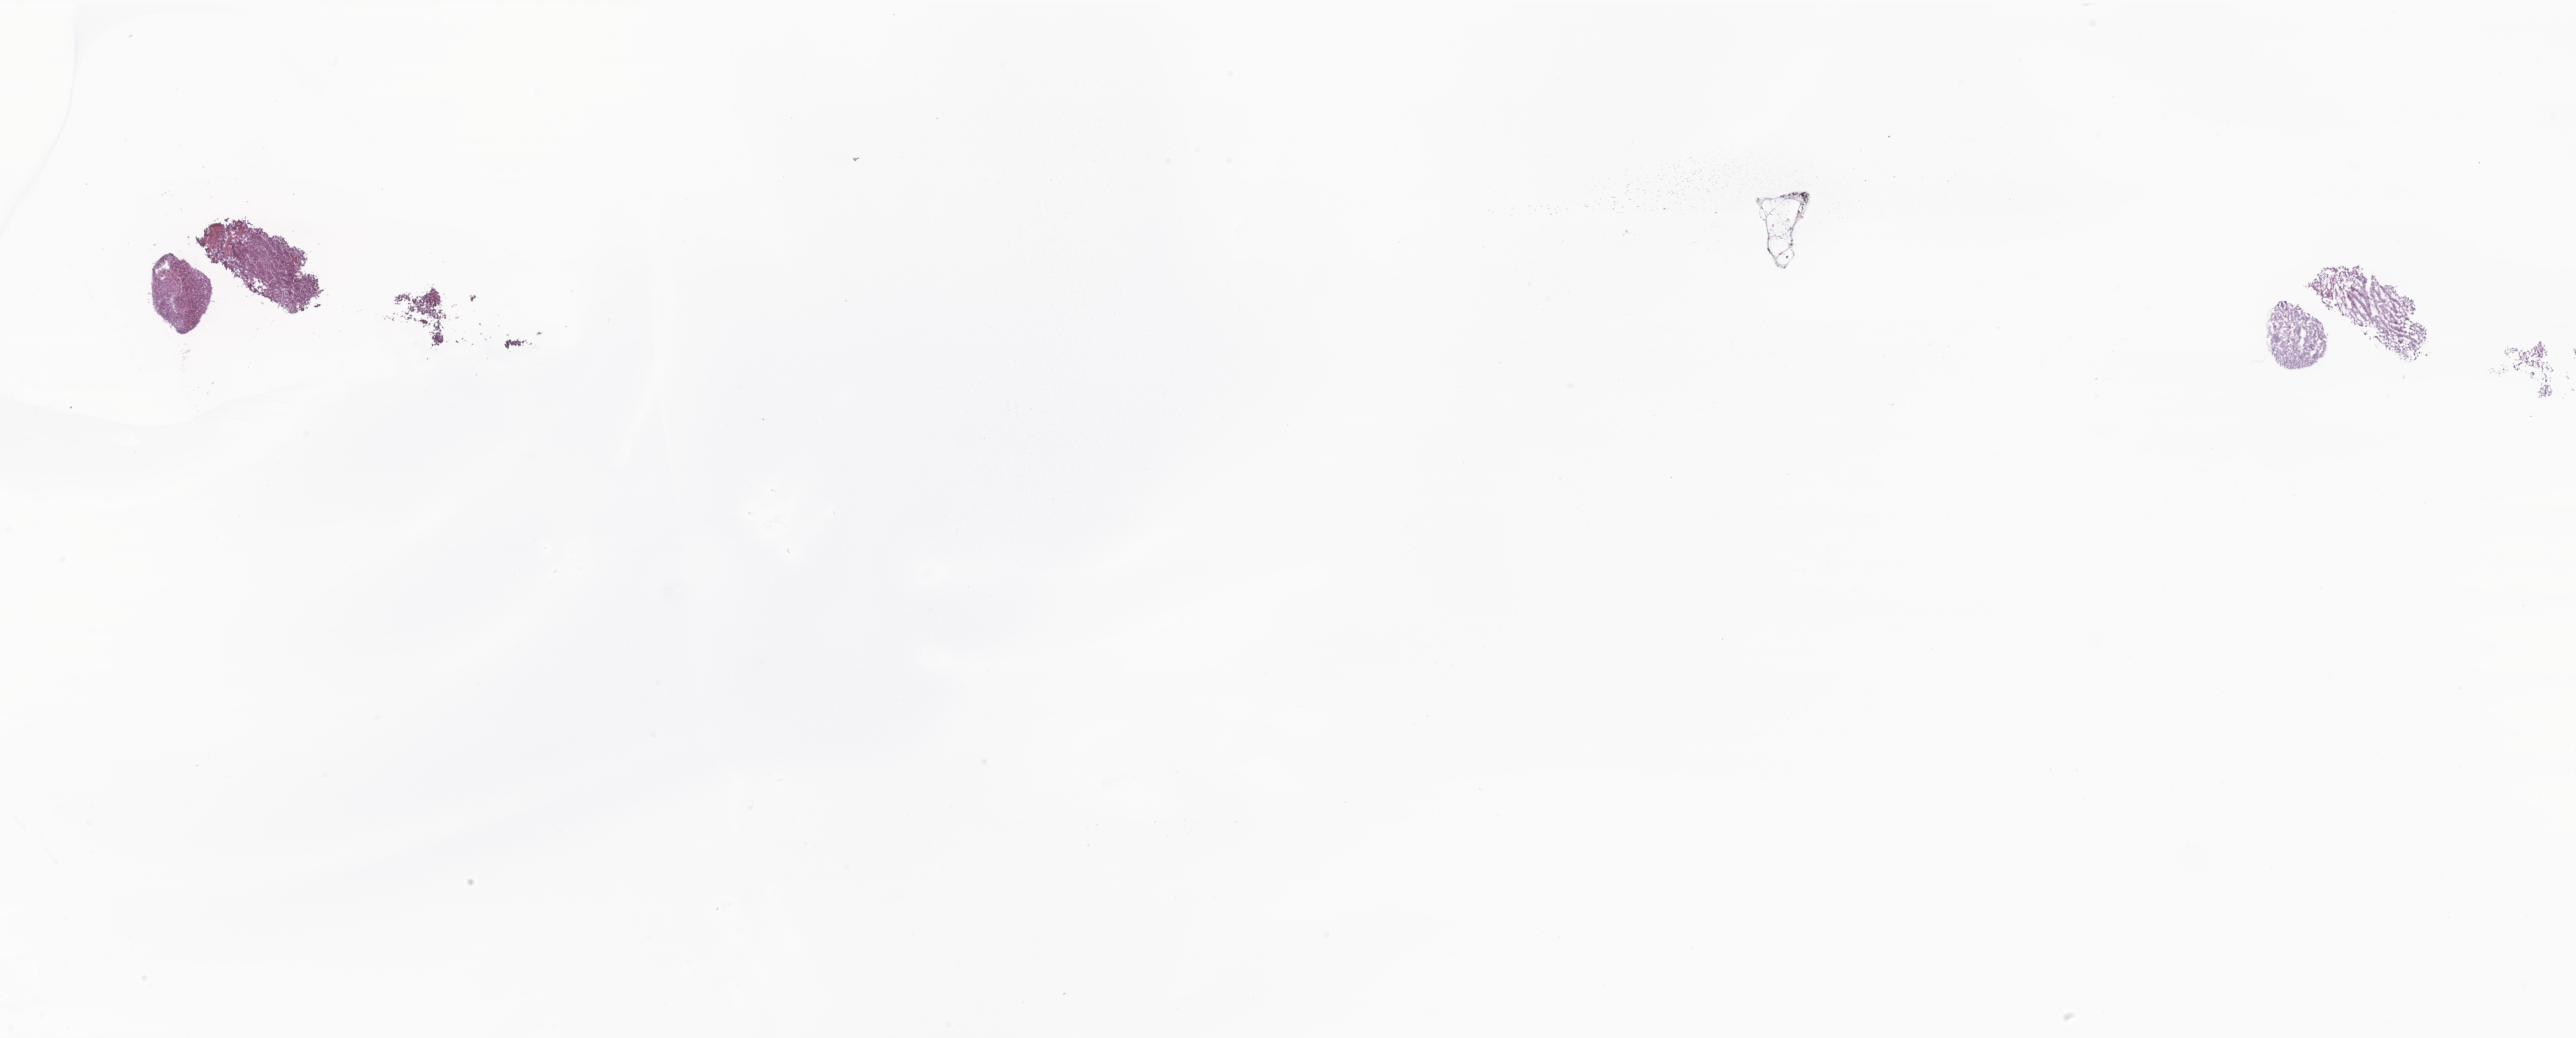
Digitized H&E-stained section of tumor tissue from the cerebellum, a low-resolution overview of the entire scanned area, about 33.7 x 13.6 mm; frozen section. Patient female; age 87 months.
Recorded diagnosis: Large cell medulloblastoma.